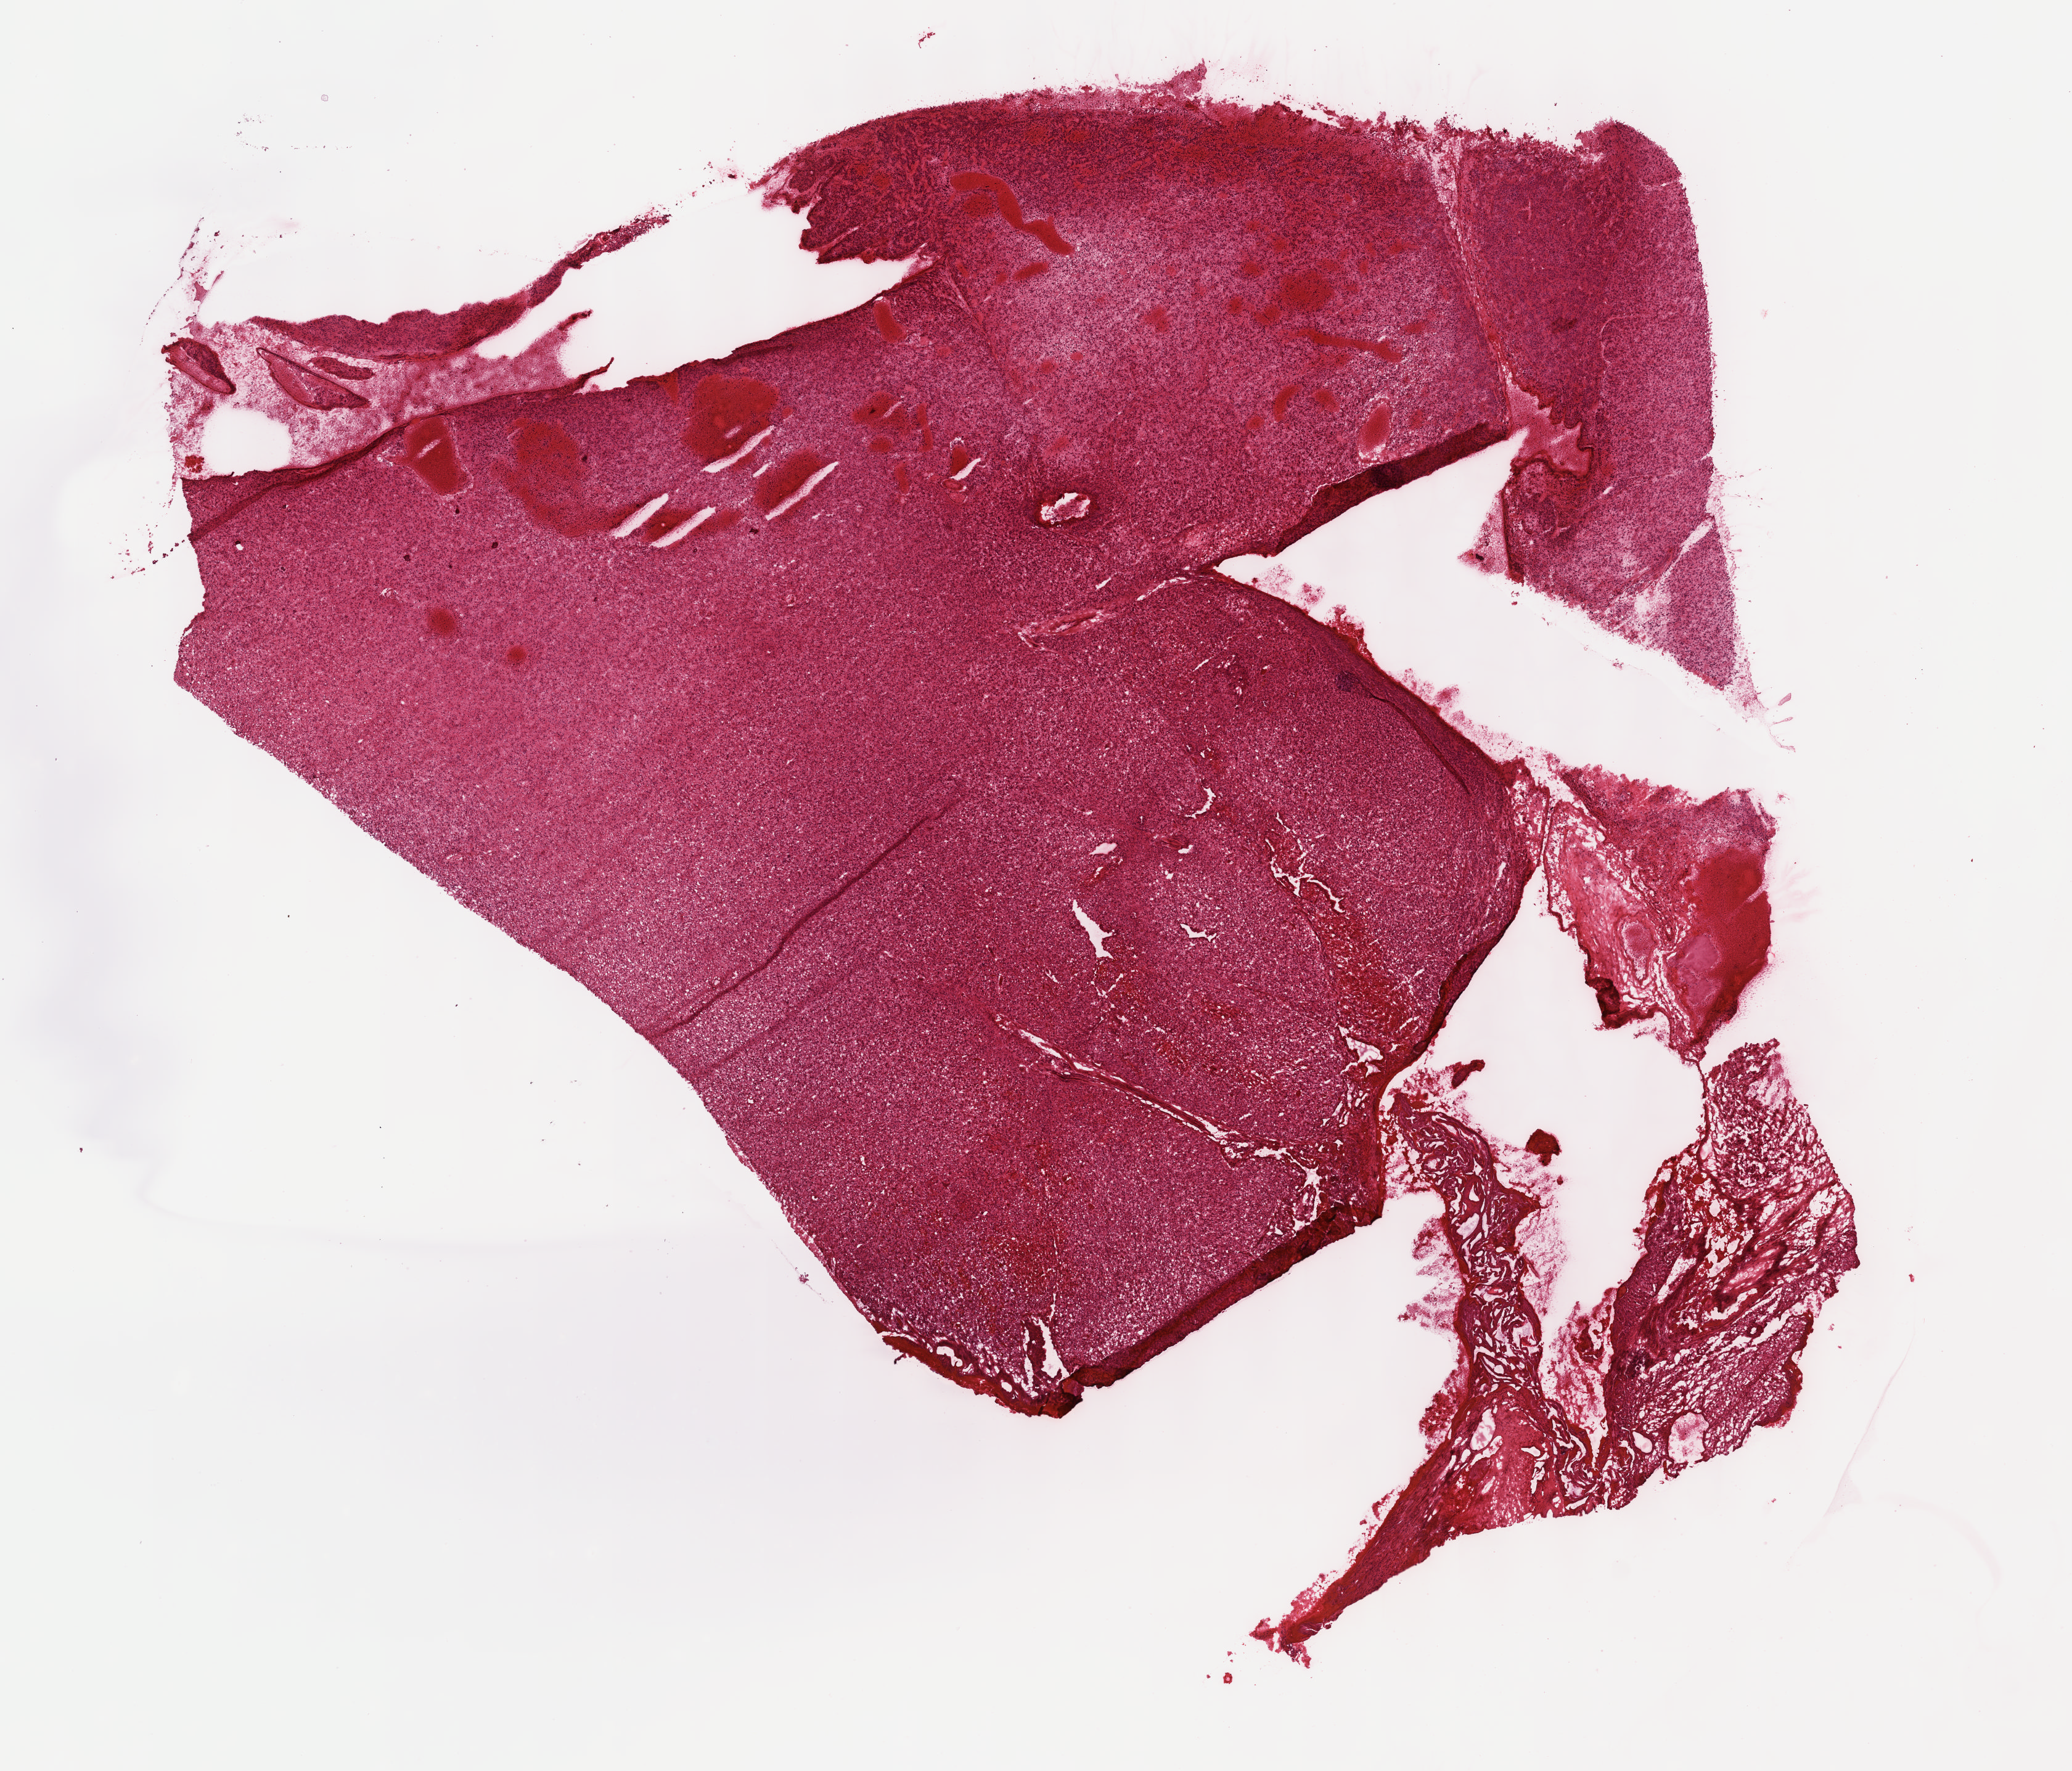
Whole-slide histology image, H&E-stained — a low-resolution overview of the entire scanned area, about 13.6 x 11.6 mm (acquisition: 40x scan). Frozen section. Primary tumour sample from the brain. Male, age 60 years at initial diagnosis. Pathologist review of this section (percent, as recorded): tumour cells 100%, tumour nuclei 100%, normal cells 0%, stromal cells 0%, necrosis 0%.
Diagnosis: Glioblastoma.